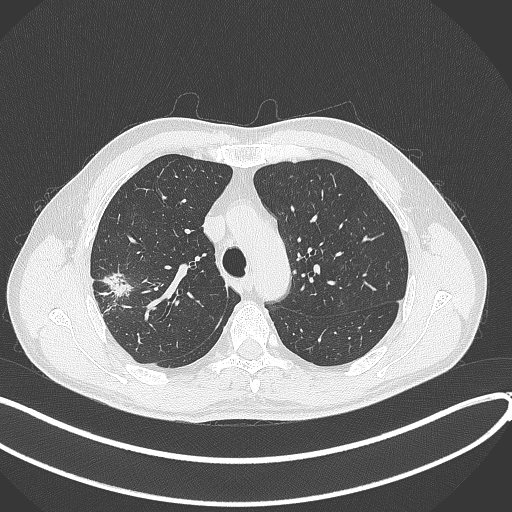
Chest CT, one axial slice; position 308 of 381 along the scan axis; reconstruction kernel B70f; 120 kVp; lung window (W 1500 / L -600 HU); 1 mm slice thickness; 512 × 512 image matrix. Patient: male, 62 years. From the clinical record (not read from this slice): clinical TNM (as recorded): T1c N0 M0.
Structures marked on this image (rectangle marked by the reading radiologist):
- lung tumour (recorded histology: adenocarcinoma): bounding box (x1, y1, x2, y2) in pixels: (99, 268, 134, 300)